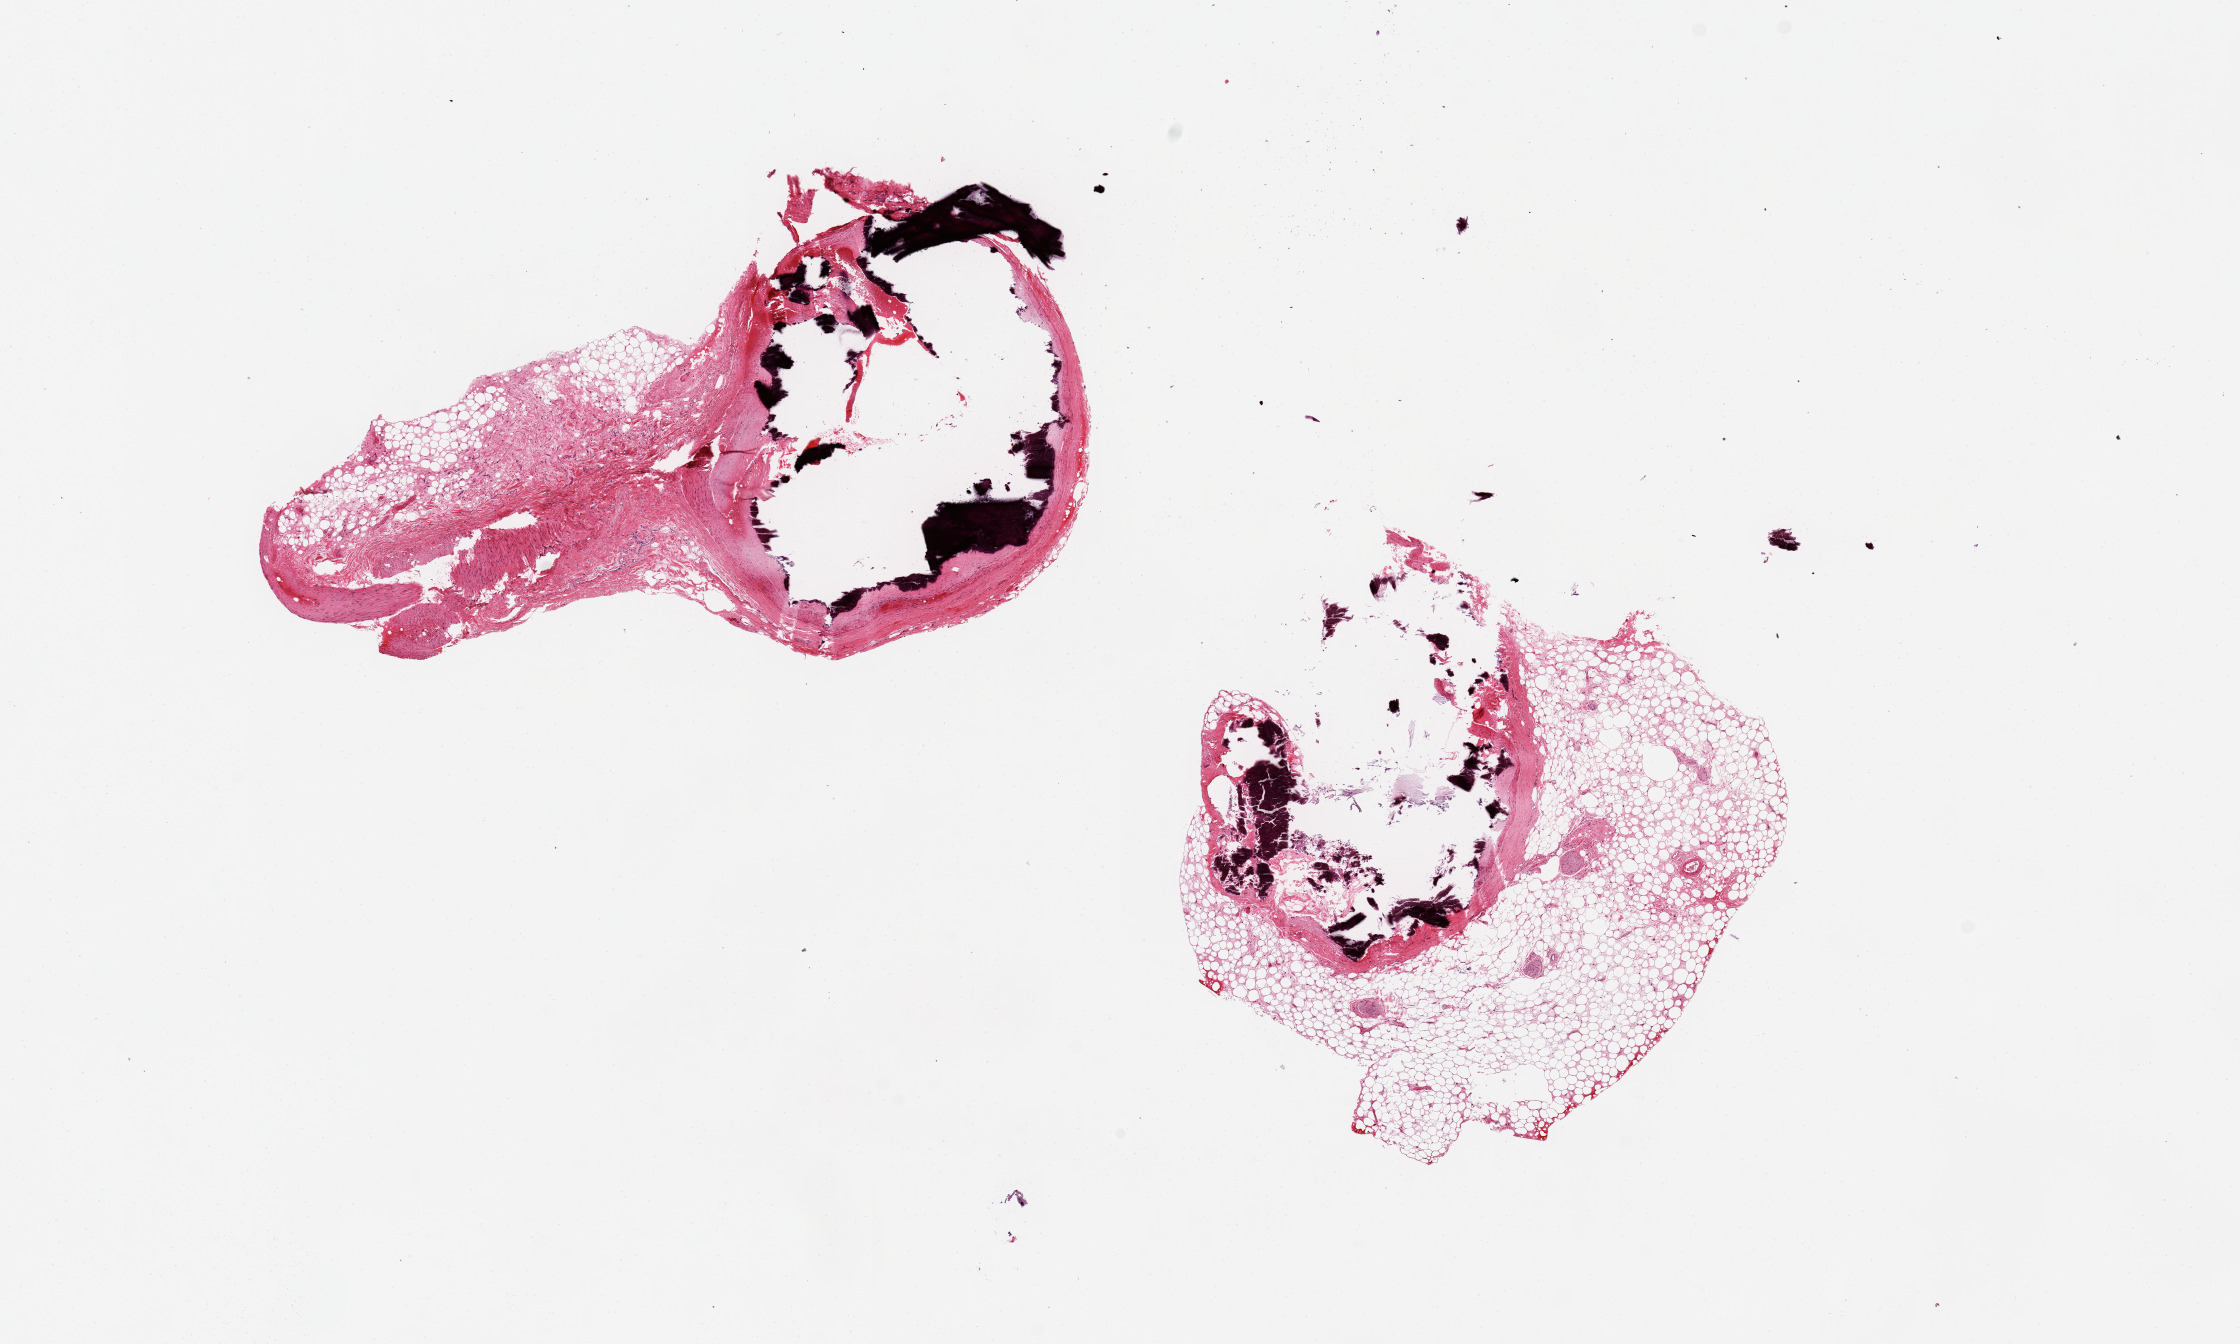
Haematoxylin and eosin whole-slide image, low-resolution overview of the scanned area, about 17.7 x 10.6 mm (slide scanned at 20x). PAXgene-fixed, paraffin-embedded tissue. Target tissue: coronary artery. Donor tissue sample. Donor: female.
Reviewer comment on this tissue sample: 2 pieces, 6x3 & 4x4 mm; both 3 mm arteries are heavily calcified; ~30-40% adjacent external adipose tissue.